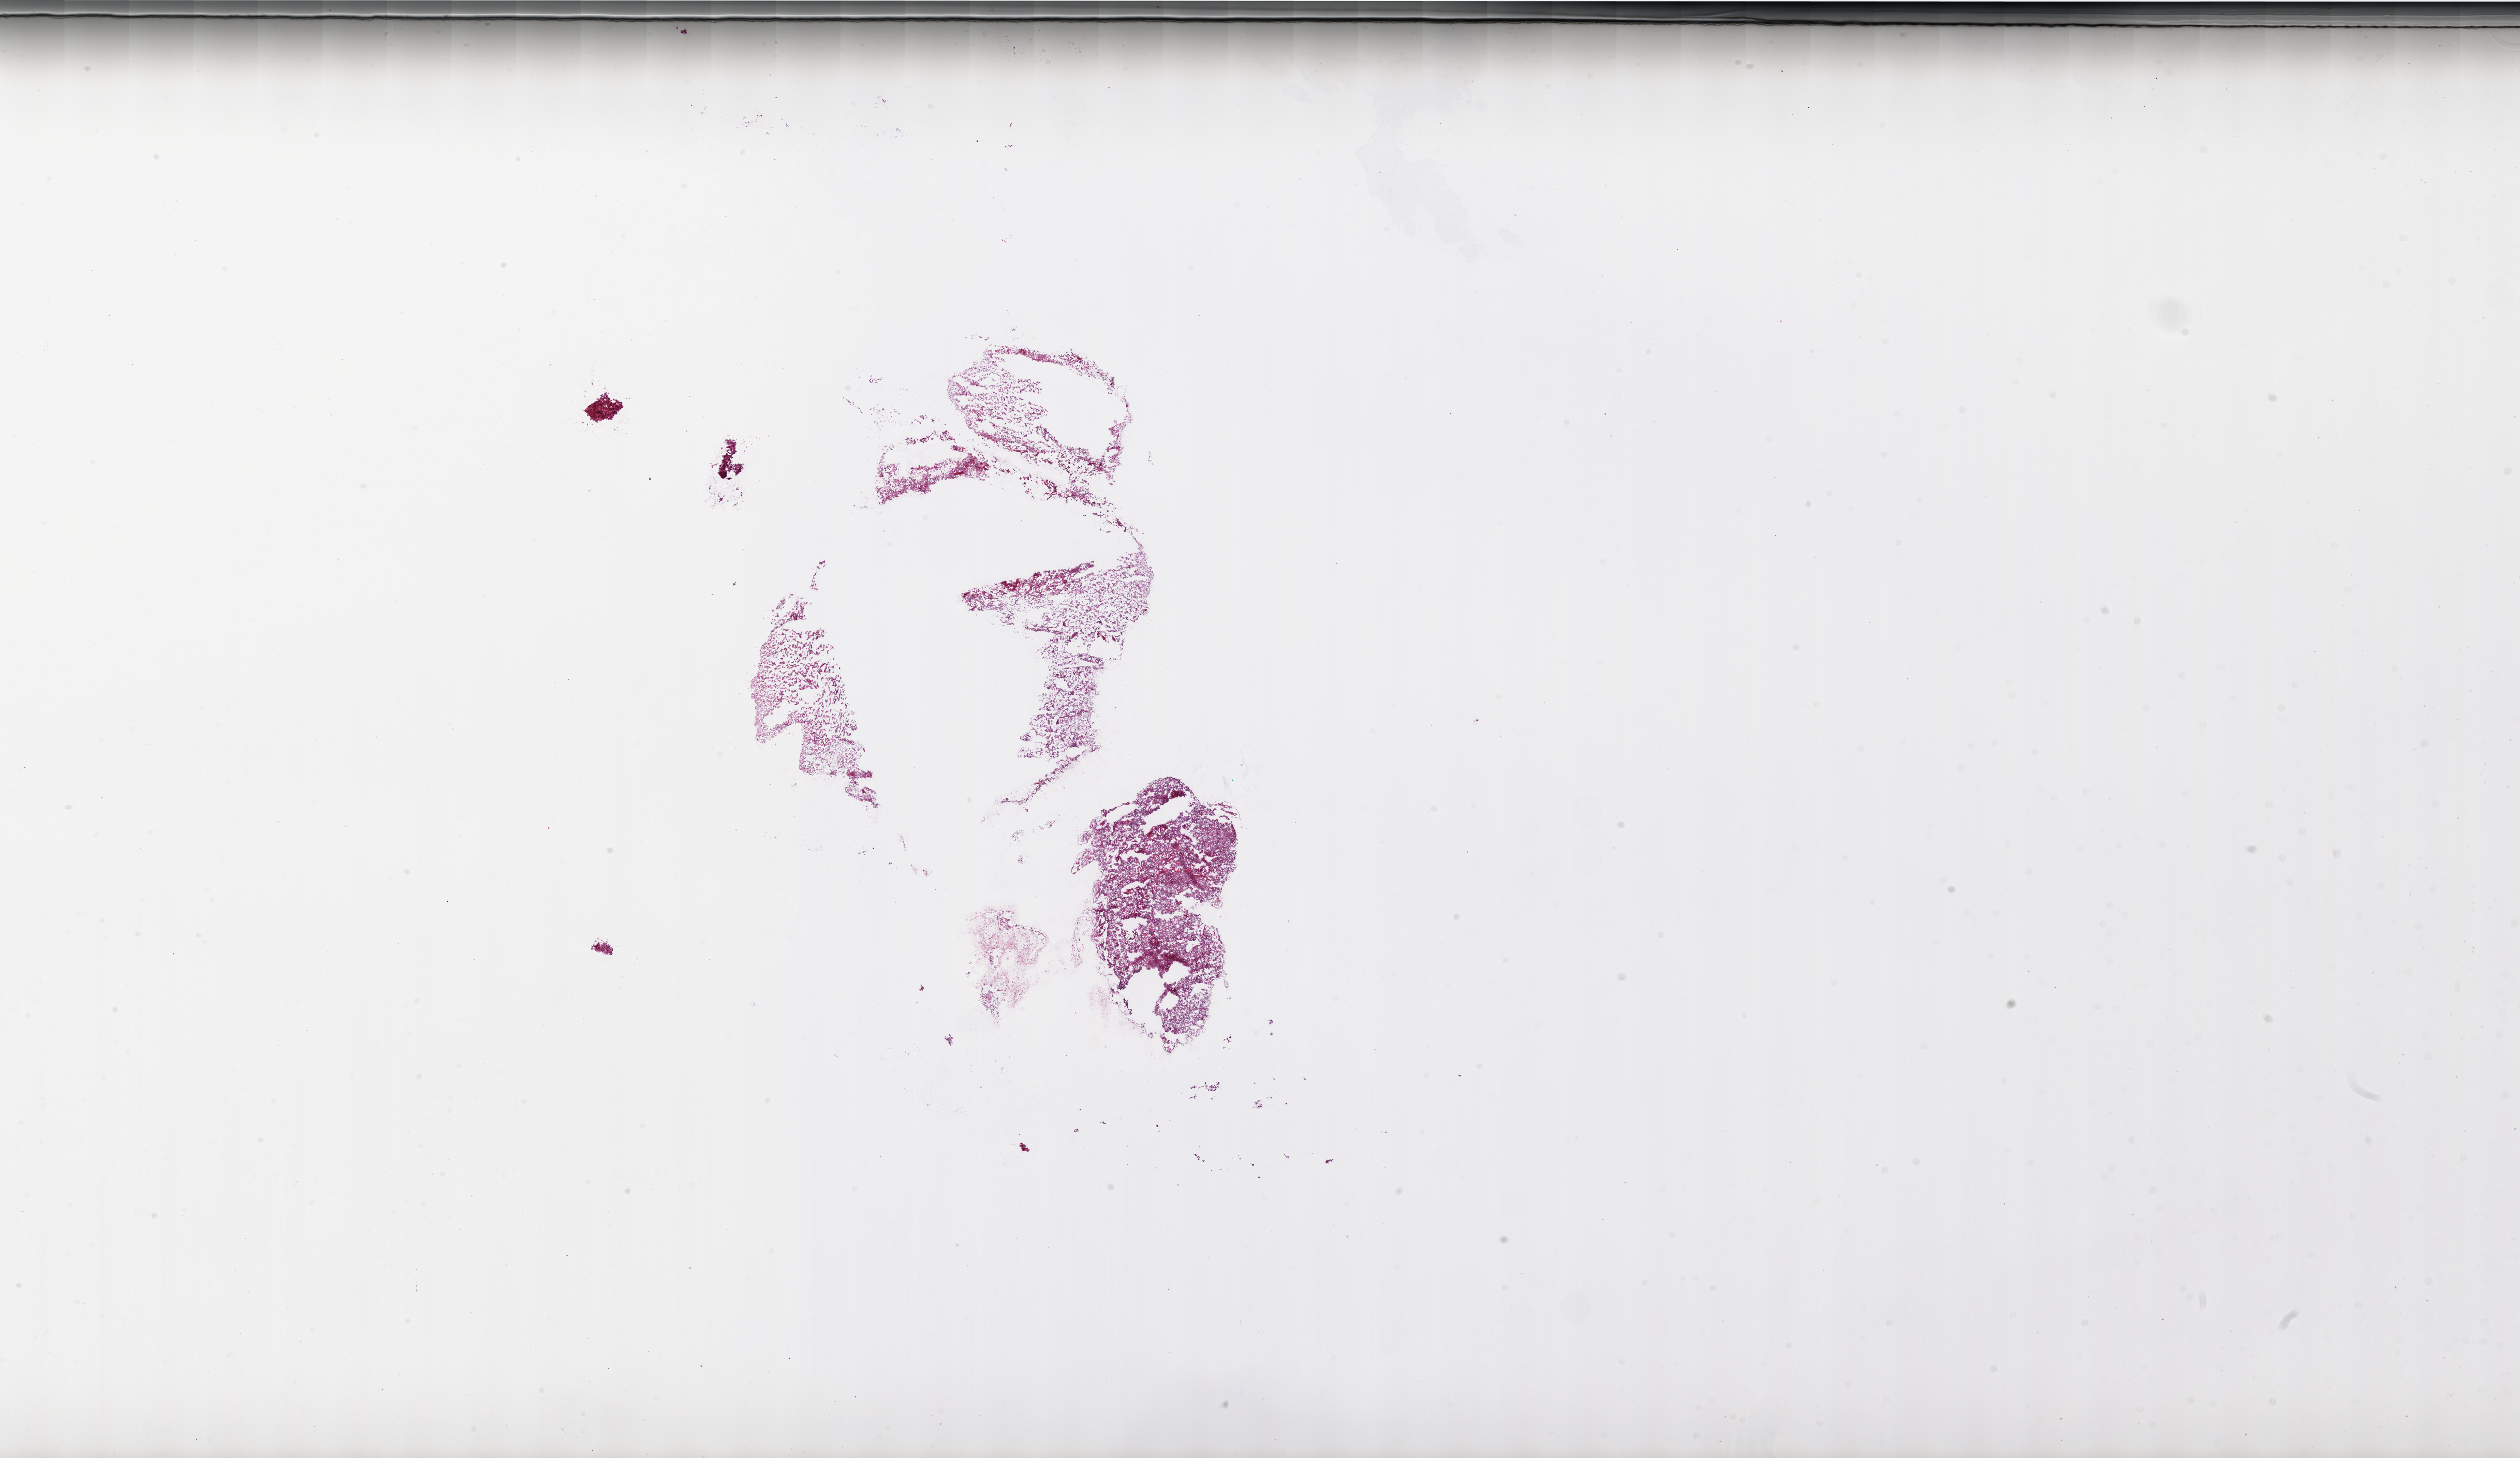
Whole-slide histology image, H&E-stained, low-resolution overview of the scanned area, about 39.0 x 22.5 mm (slide scanned at 20x). Frozen section from the bottom of the tissue portion. Sample: primary tumour, brain. Patient: male, age at initial diagnosis 49 years. Composition of this section per pathologist review: tumour cells 90%, tumour nuclei 100%, normal cells 0%, stromal cells 0%, necrosis 10%. Infiltration values recorded for this section: lymphocyte infiltration 0%.
Diagnosis: Glioblastoma.